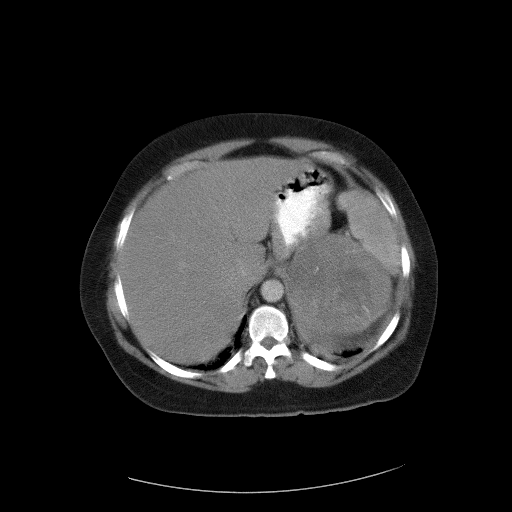
Contrast-enhanced abdominal CT, one axial slice. Slice 79 of 90 in the series (ordered by position). 120 kVp. Soft-tissue window (W 400 / L 40 HU). 5 mm slice thickness. 512 × 512 image matrix, field of view 480 × 480 mm. Female patient, age 55 years. Case-level facts recorded for this patient, not image findings: diagnosis: adrenocortical carcinoma; tumour side: left adrenal; tumour size at pathology: 22 cm; Ki-67 index: 10 %; stage (as recorded): 3.
Outlined on this slice (semi-automatically segmented with operator editing):
- mass: bounding box [x1, y1, x2, y2] px = [293, 234, 389, 335]